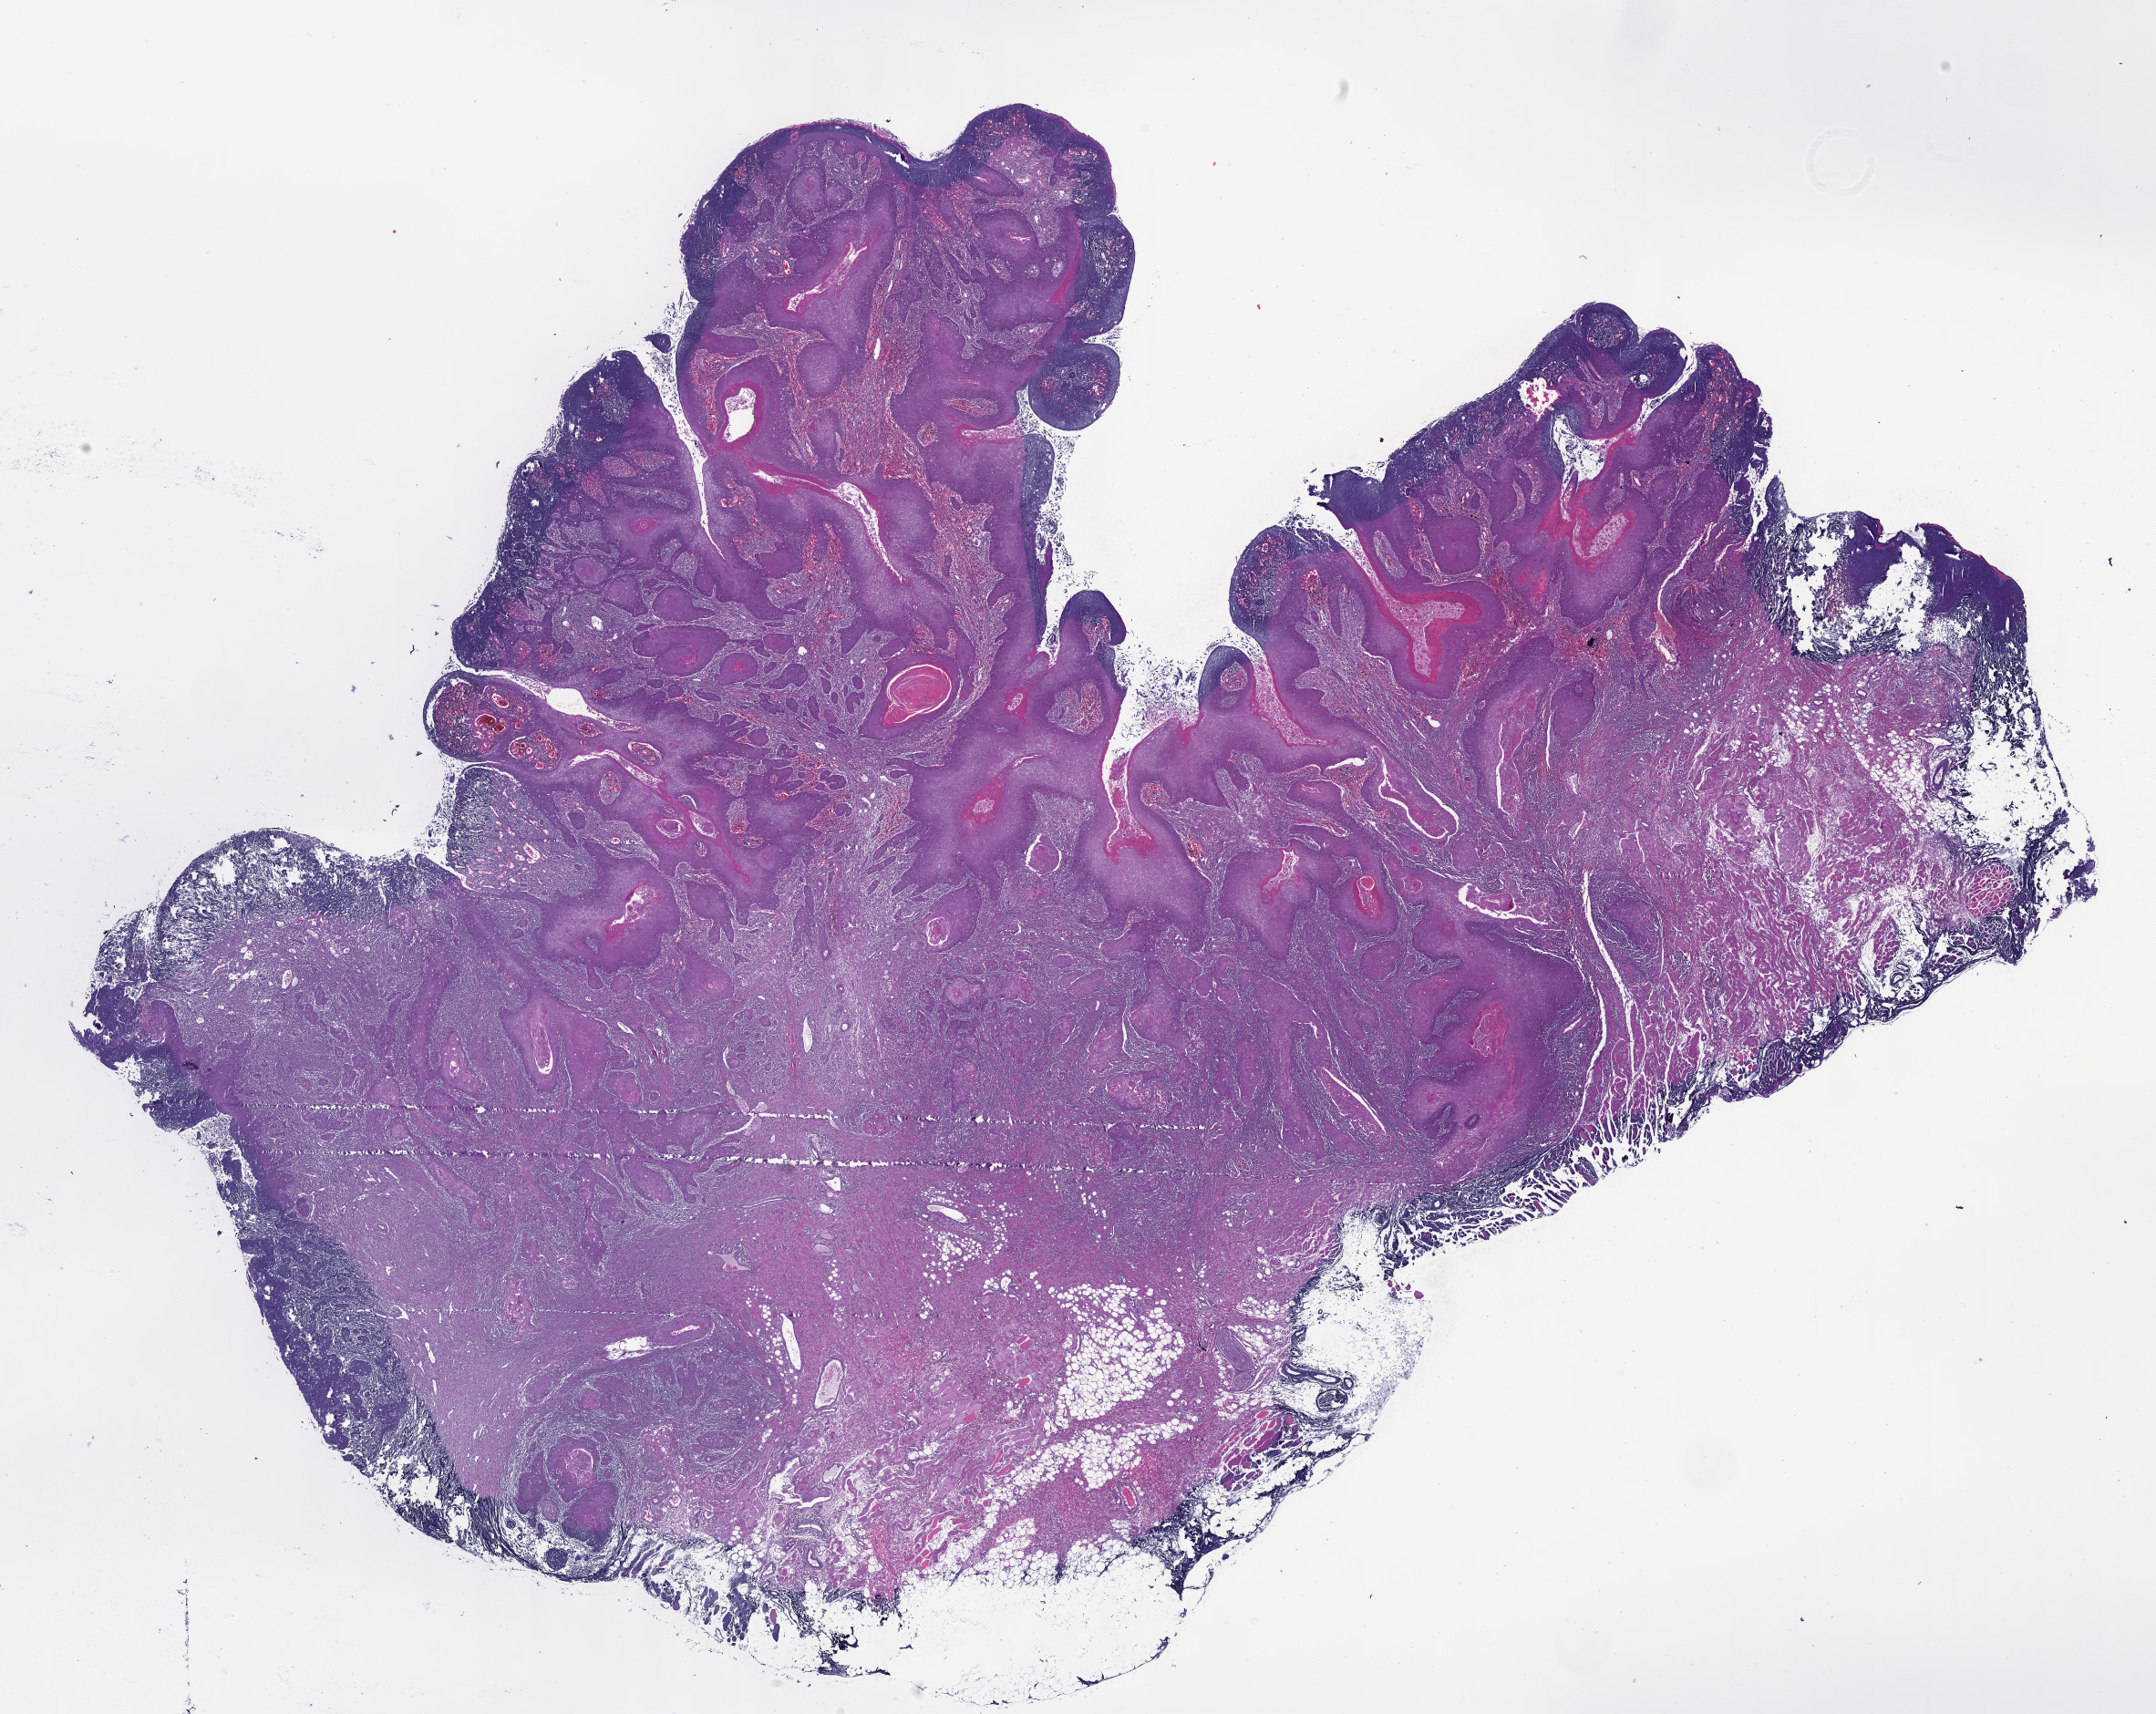
Digitized H&E tissue section (whole slide) — low-resolution overview of the scanned area, about 19.1 x 15.2 mm (slide scanned at 40x), FFPE section, head and neck, primary tumour sample. Patient: female, age at initial diagnosis 69 years.
Diagnosis: Squamous cell carcinoma, NOS (mouth, NOS).